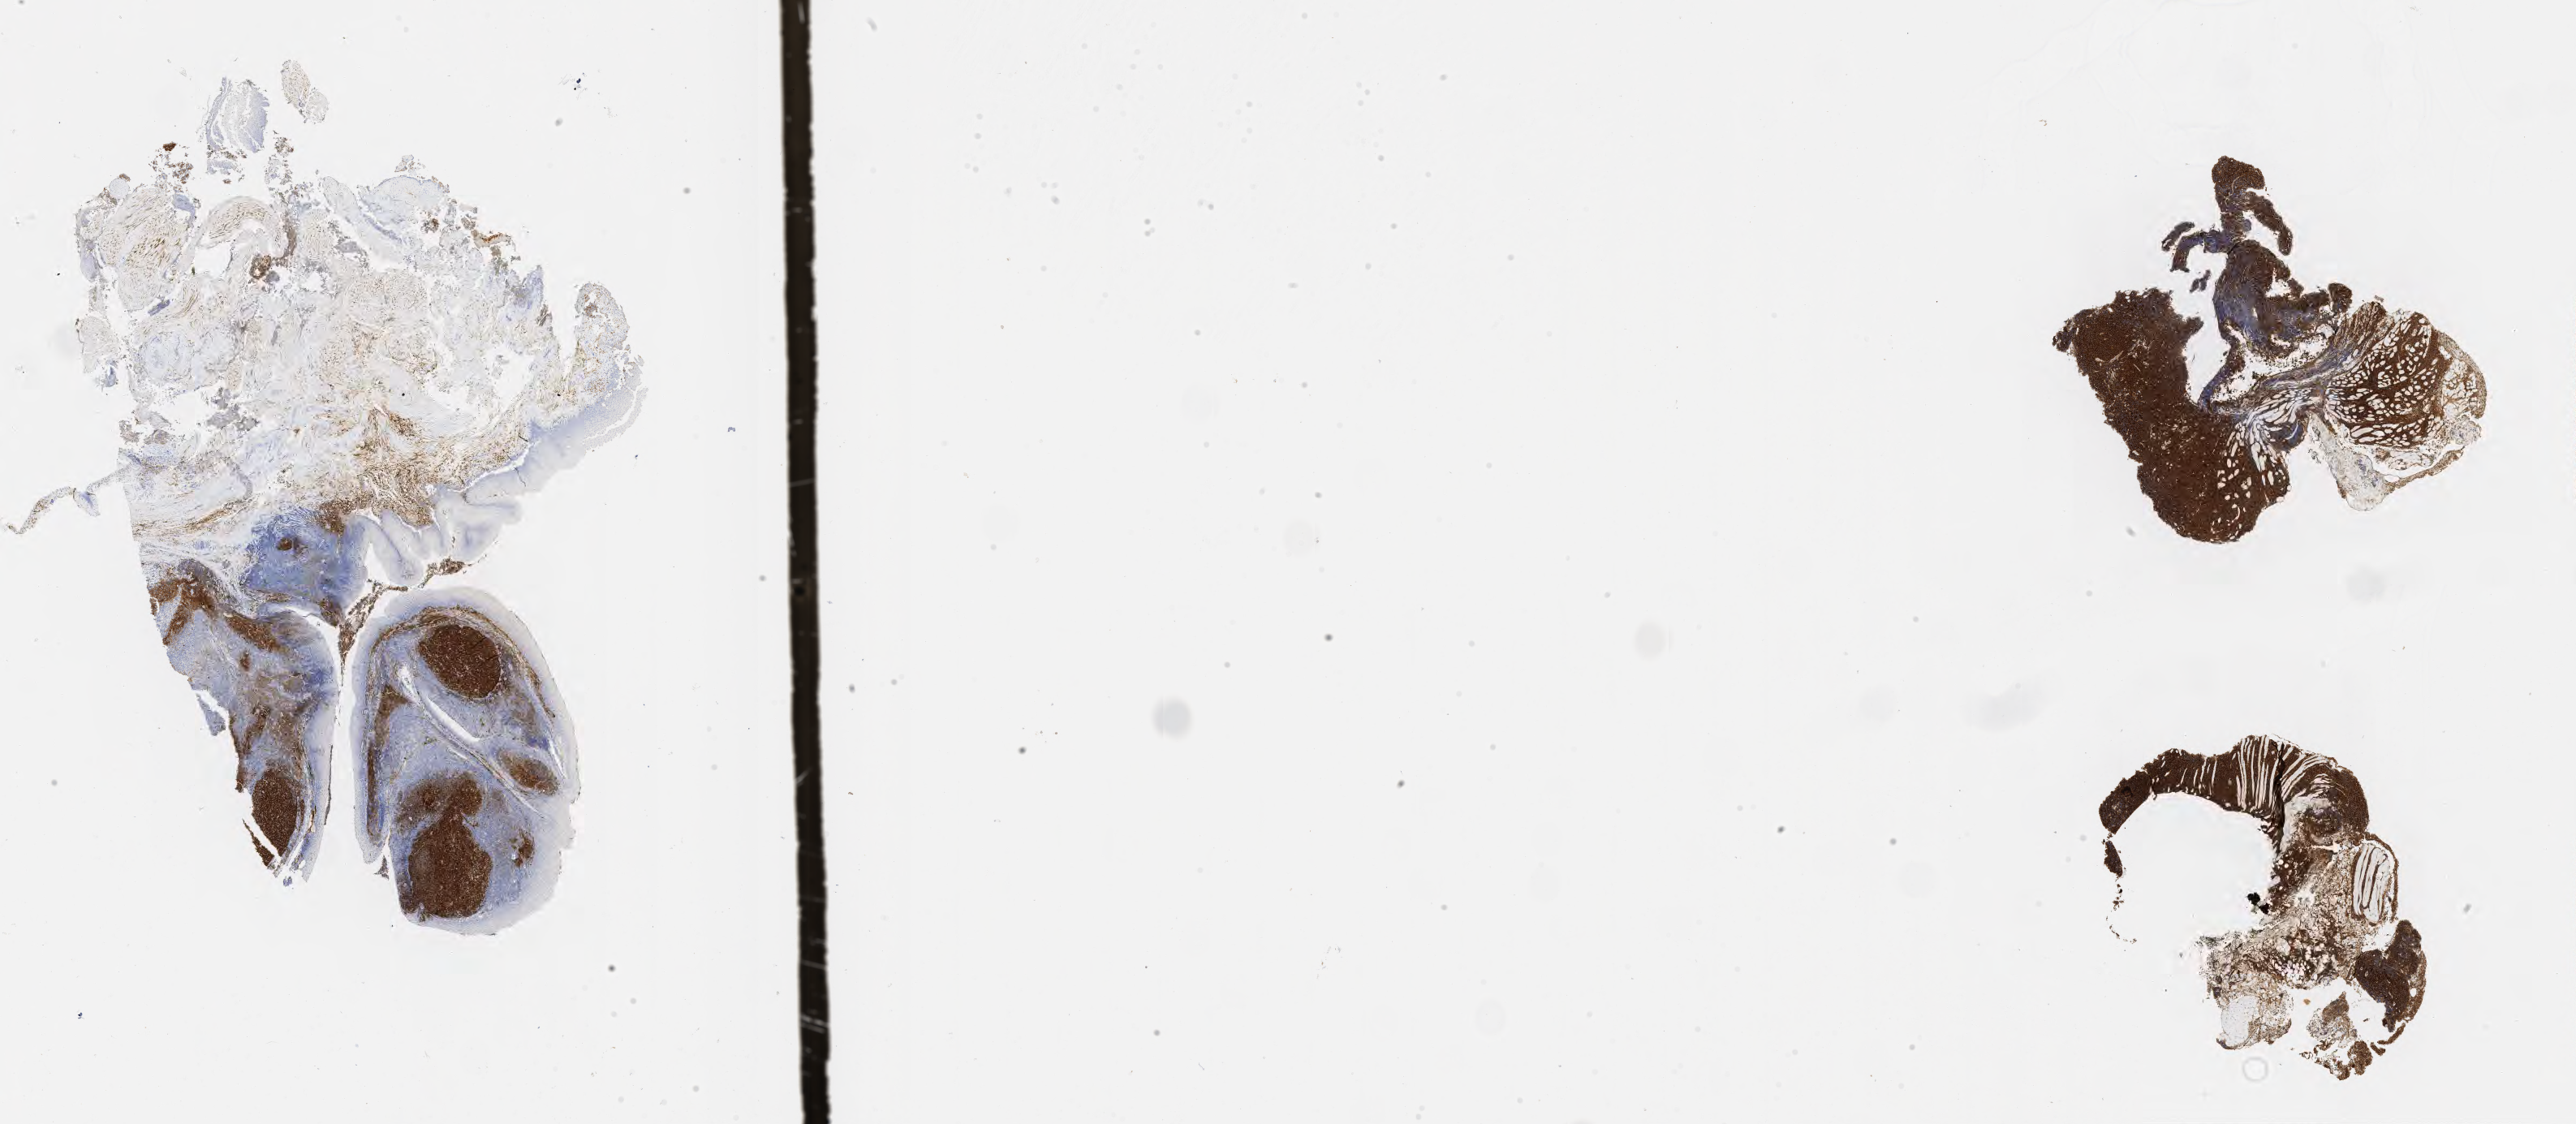
IHC for CD10, whole-slide image, low-resolution overview of the scanned area, about 25.7 x 11.2 mm; specimen: tumor tissue; anatomic site: lymph node of head and neck. Patient male; aged 73.
Histologic diagnosis: Burkitt lymphoma, NOS.